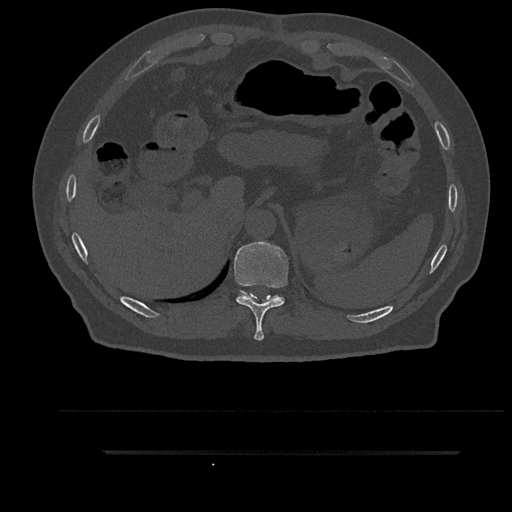
CT including the spine, one axial slice. Slice 350 of 797 in the series (ordered by position). 120 kVp. Bone window (W 1800 / L 400 HU). 0.5 mm slice thickness. 512 × 512 image matrix. Male patient, age 63 years. Case-level facts recorded for this patient, not image findings: primary cancer: renal; vertebrae with lytic lesions (as recorded): T8.
Annotated regions visible in this slice (semi-automatically segmented with operator editing):
- T10 vertebra: bounding box (x1, y1, x2, y2) in pixels: (234, 242, 288, 341)
- T11 vertebra: (239, 290, 279, 299)